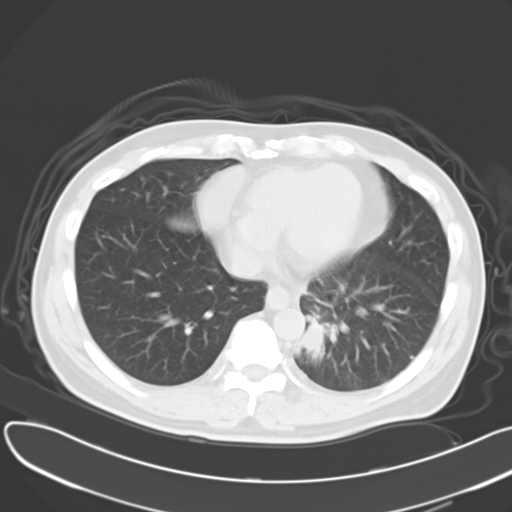
Chest CT, one axial slice; reconstruction kernel B40f; 120 kVp; lung window (W 1500 / L -600 HU); 512 × 512 image matrix, field of view 376 × 376 mm. Male patient, age 55 years. Case-level facts recorded for this patient, not image findings: clinical TNM (as recorded): T2 N3 M0; histopathological grade: G3.
Structures marked on this image (rectangle marked by the reading radiologist):
- lung tumour (recorded histology: small cell carcinoma): bounding box <295,306,329,360> (left, top, right, bottom; pixels)